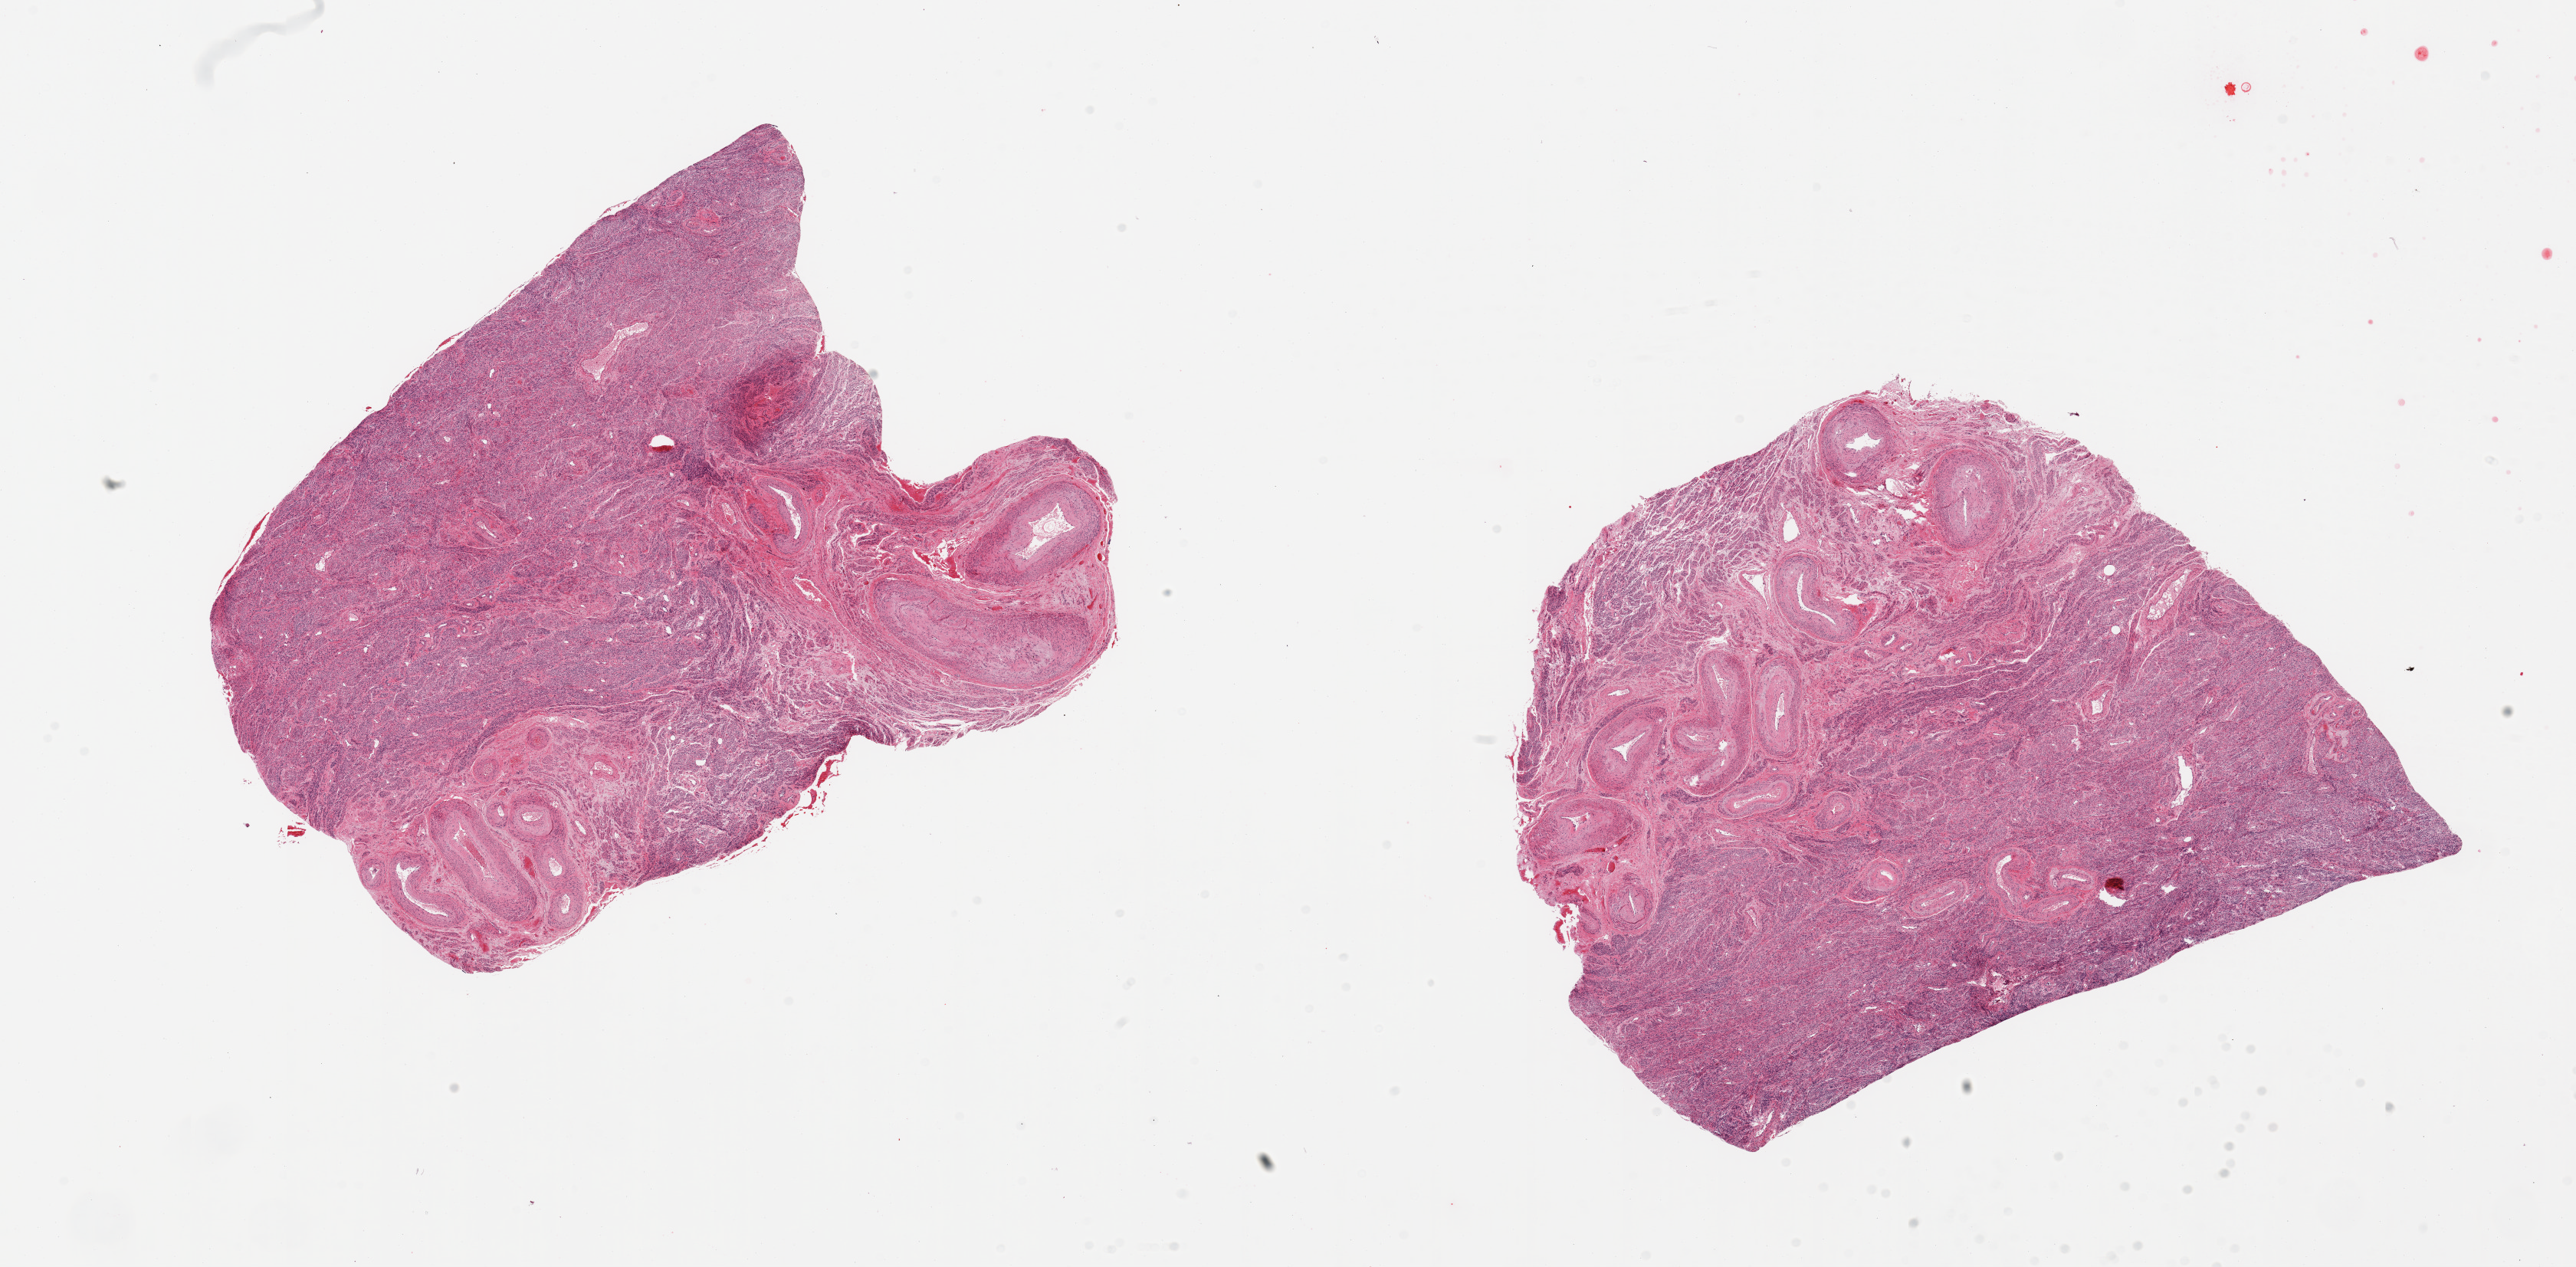
H&E whole-slide image — shown as a low-resolution overview of the whole scanned area (about 26.6 x 13.1 mm, slide scanned at 20x); PAXgene-fixed, paraffin-embedded tissue; target tissue: uterus; tissue donor sample. Female donor.
• review note (as recorded): 2 pieces, all myometrium, no abnormalities